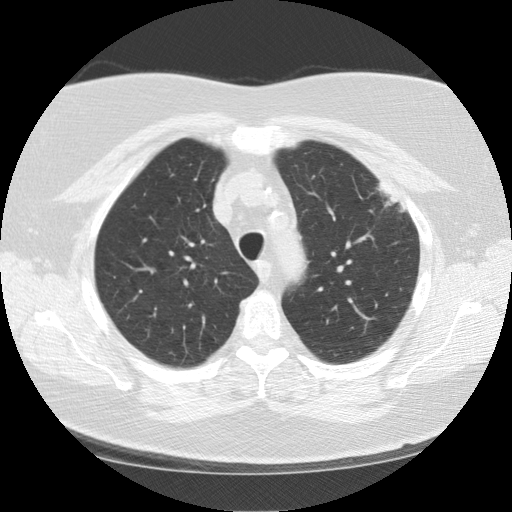
Low-dose screening chest CT, one axial slice; slice 101 of 130 in the series (ordered by position); lung window (W 1500 / L -600 HU); 2.5 mm slice thickness; 512 × 512 image matrix, field of view 350 × 350 mm.
Outlined on this slice (manually delineated by an expert):
- lesion 1 (tumor, upper lobe of left lung): bounding box <377,182,407,212> (left, top, right, bottom; pixels)